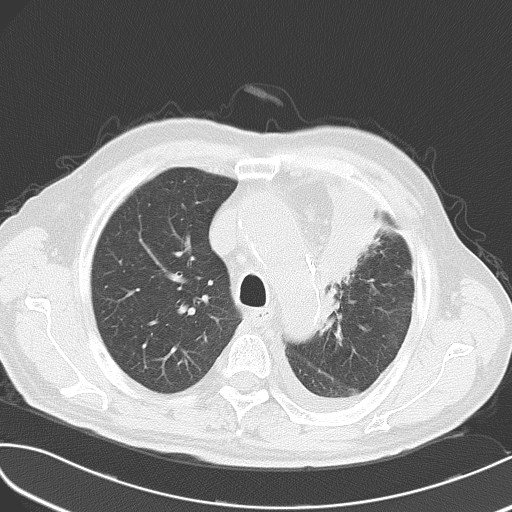
Chest CT, one axial slice. Position 41 of 54 along the scan axis. Reconstruction kernel B70f. Lung window (W 1500 / L -600 HU). 5 mm slice thickness. 512 × 512 image matrix, field of view 353 × 353 mm. Male patient, age 70 years. From the clinical record (not read from this slice): clinical TNM (as recorded): T2 N1 M3; histopathological grade: G3.
Structures marked on this image (rectangle marked by the reading radiologist):
- lung tumour (recorded histology: small cell carcinoma): bounding box <312,171,390,295> (left, top, right, bottom; pixels)